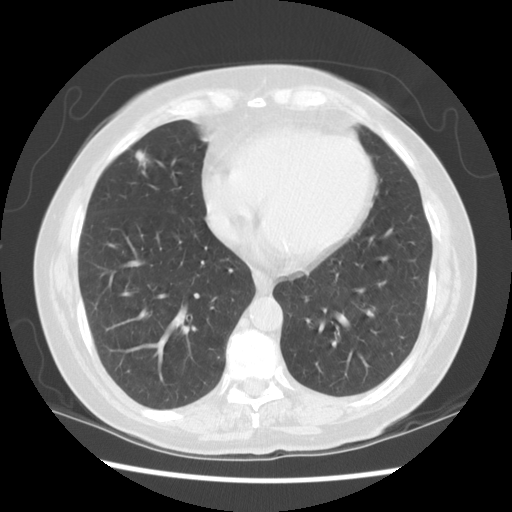
Low-dose screening chest CT, axial slice; second screening round (one year after baseline); lung window (W 1500 / L -600 HU); 2.5 mm slice thickness; standard (soft-tissue) reconstruction kernel (STANDARD). Female participant, aged 71 years at enrolment. Current smoker at enrolment.
Expert-annotated lung lesion, bounding box (x1, y1, x2, y2) in pixels: (107, 135, 168, 190). The exam's reader record, not a measurement of the box and not confirmed to be the same lesion: non-calcified nodule or mass ≥4 mm, right middle lobe, 6 × 6 mm, spiculated (stellate) margins, soft tissue attenuation, pre-existing on the prior screen: yes; interval growth: yes. Later outcome: lung cancer diagnosed 68 days after this screen — adenocarcinoma, NOS, right middle lobe, moderately differentiated (G2), stage IA (AJCC 6th edition), 12 mm at pathology.